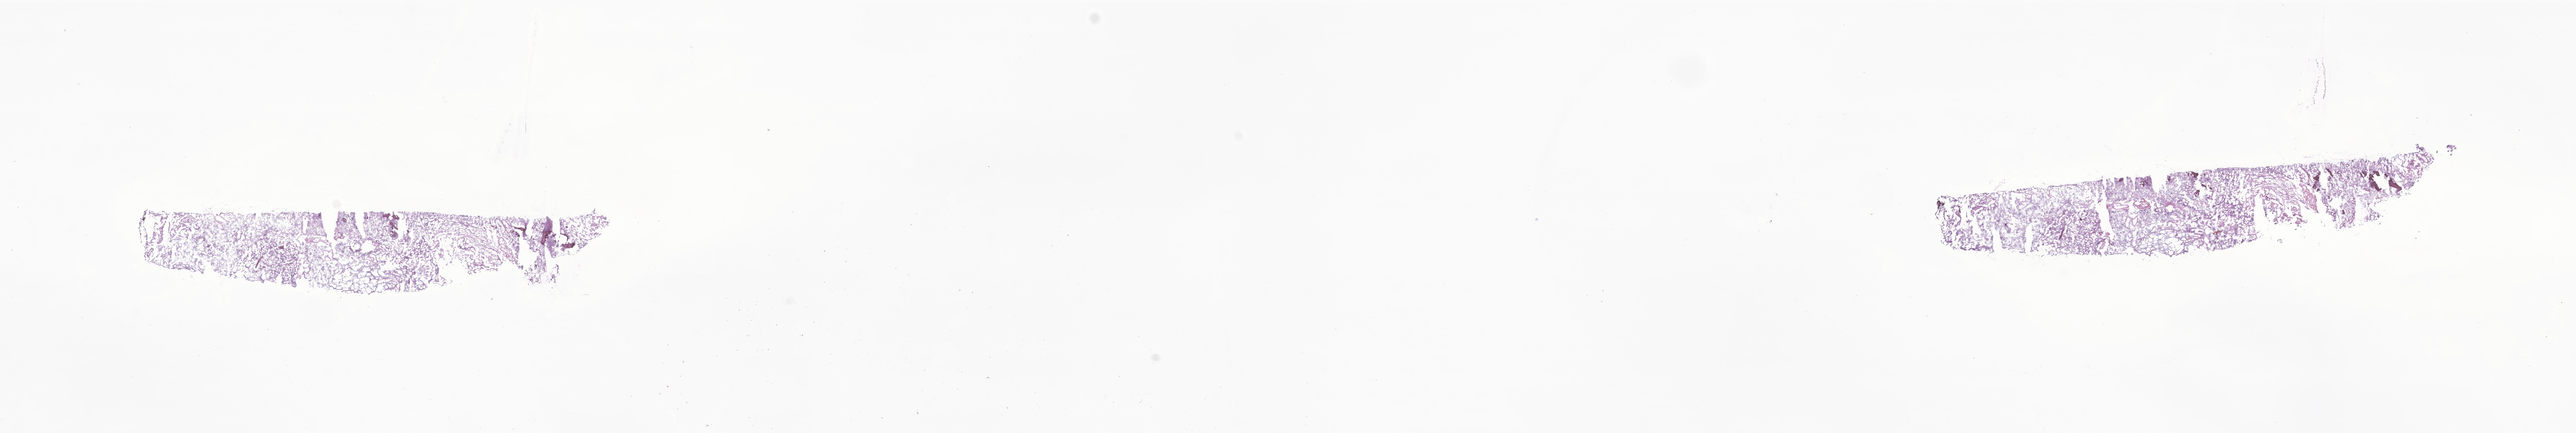
Whole-slide image, H&E stain of tumor tissue from the spinal cord, low-resolution overview of the scanned area, about 33.9 x 5.7 mm, cryosection (OCT / tissue freezing medium). Patient male; age 169 months (14 years 1 month).
- diagnosis (ICD-O-3 morphology term): Neoplasm, malignant